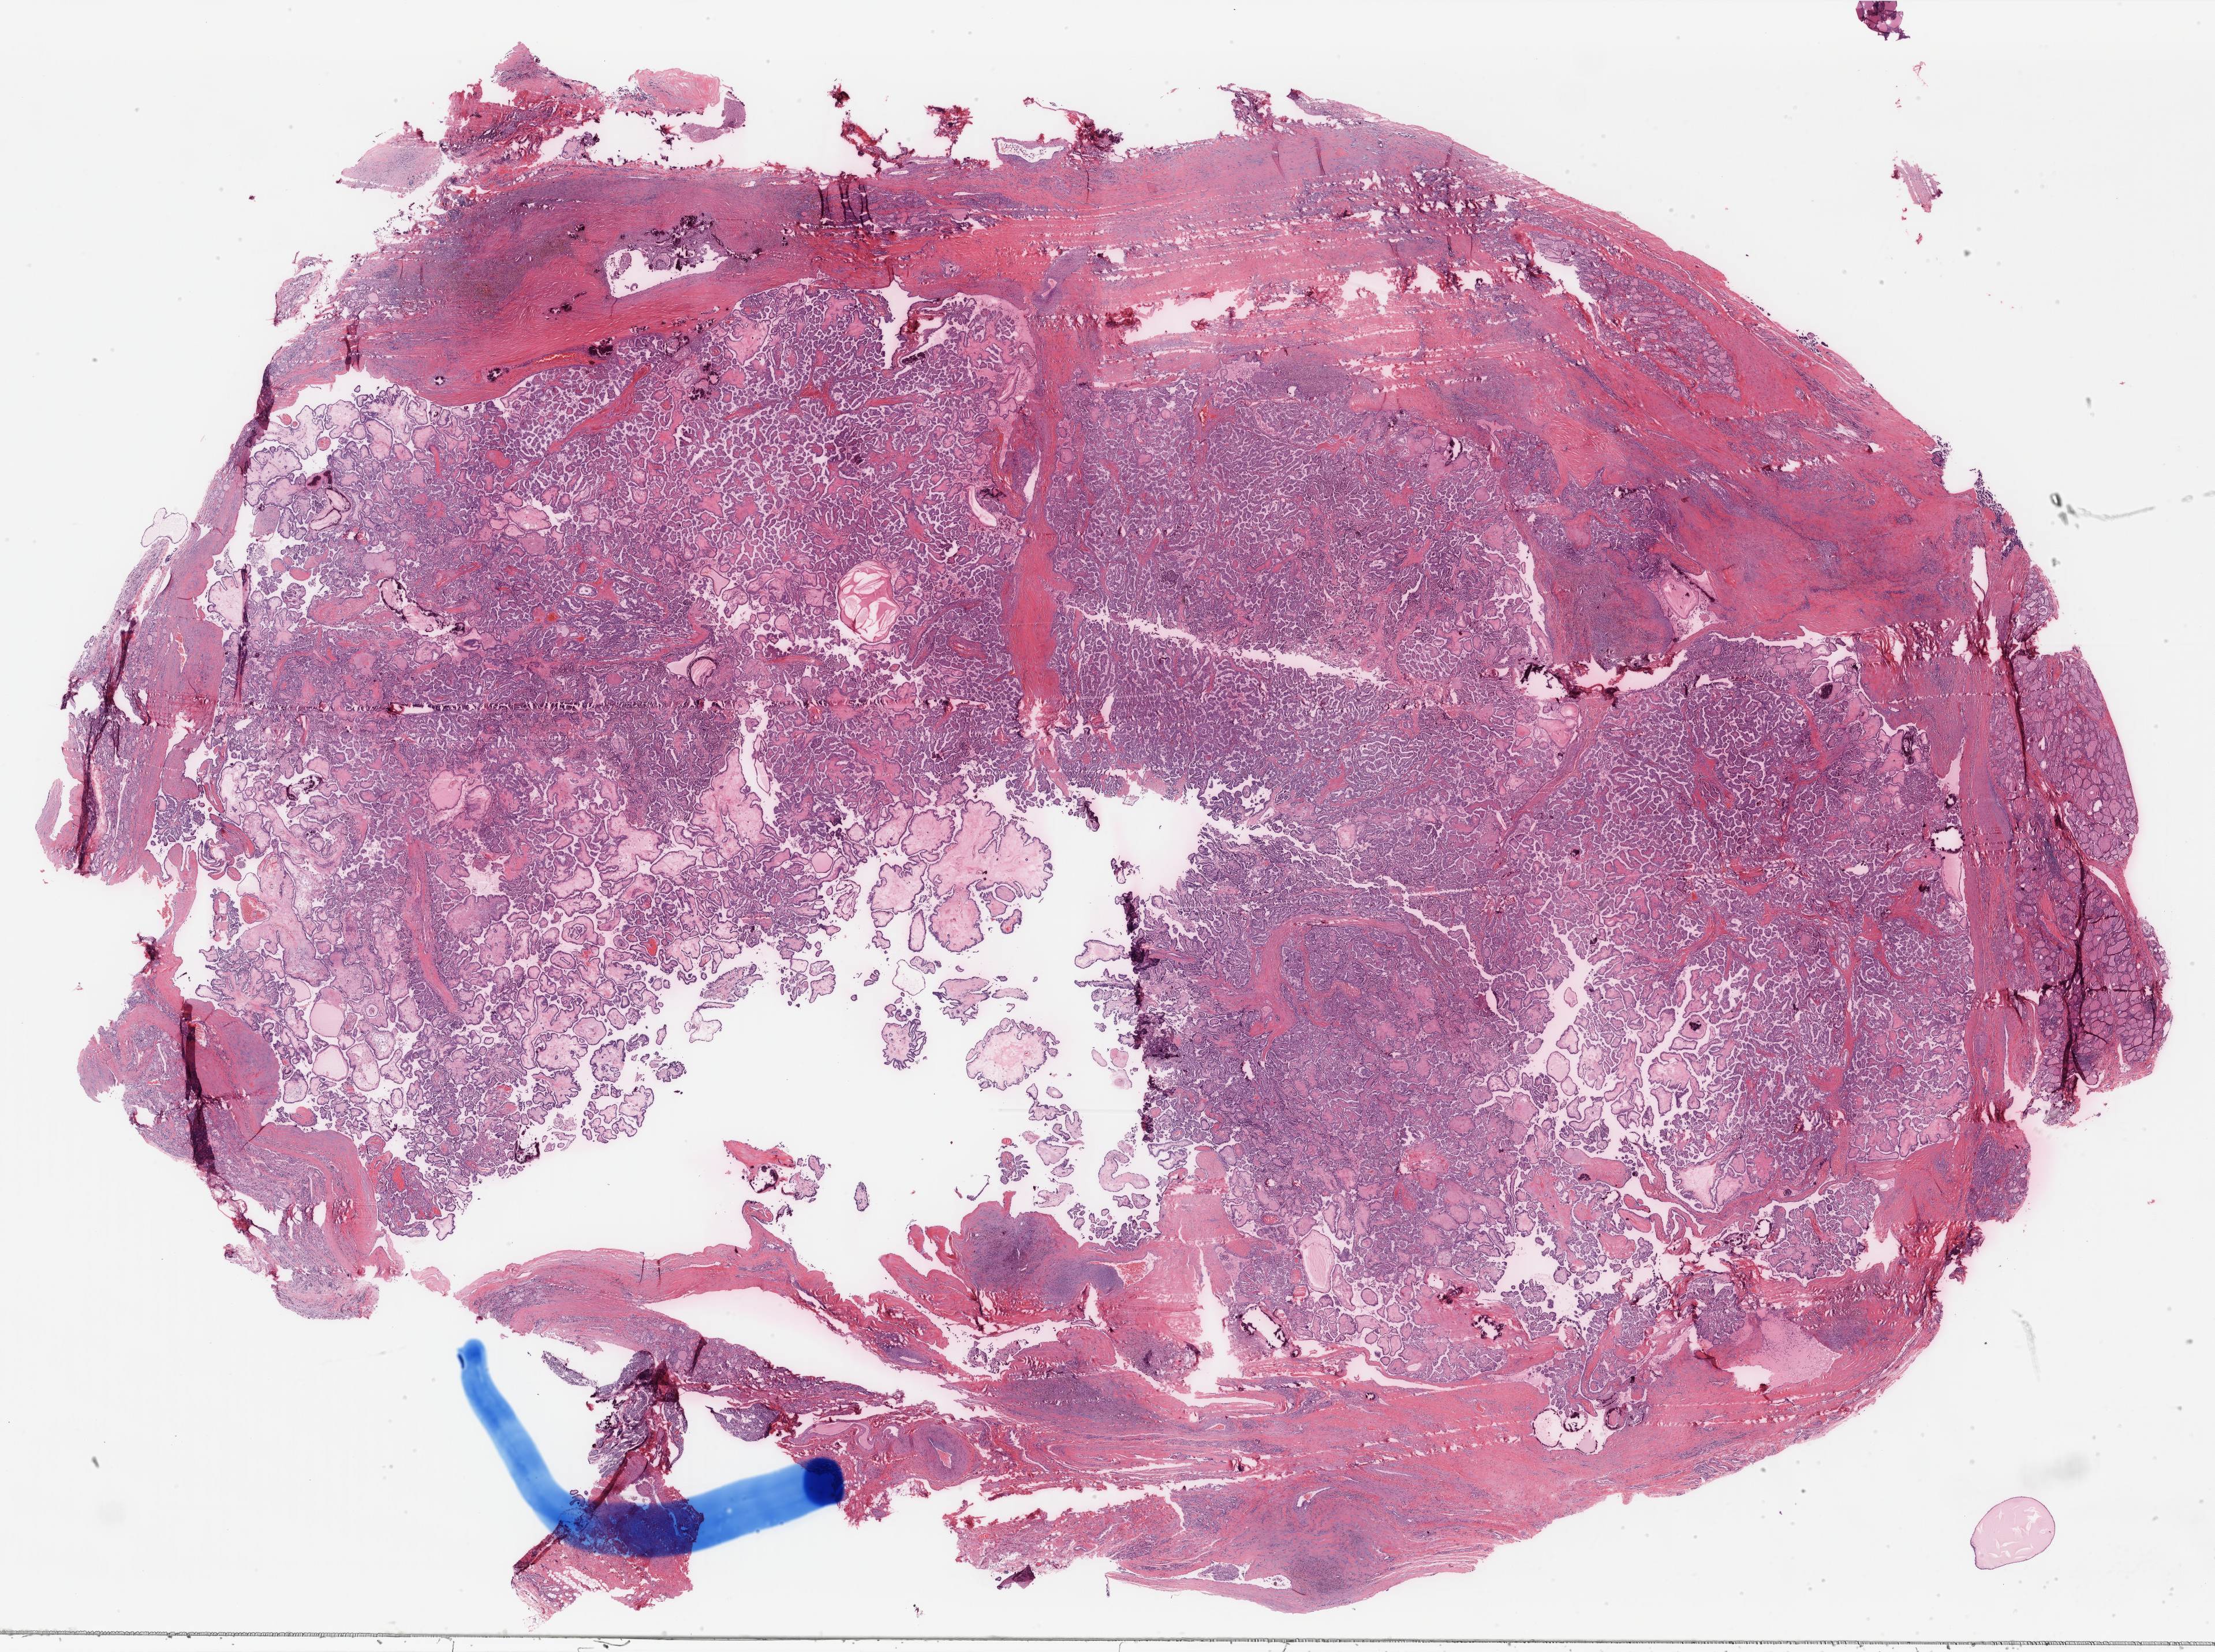
Hematoxylin and eosin (H&E) stained whole-slide image, shown as a low-resolution overview of the whole scanned area (about 30.5 x 22.7 mm). Formalin-fixed paraffin-embedded (FFPE) diagnostic section. Primary tumour sample from the thyroid. Male patient; age at initial diagnosis 39 years.
- AJCC pathologic stage: I (6th edition)
- pathologic diagnosis: Papillary adenocarcinoma, NOS (thyroid gland)